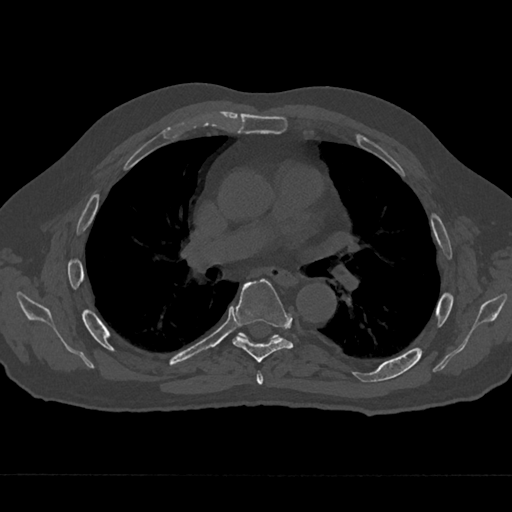
CT including the spine, one axial slice; slice 415 of 797 in the series (ordered by position); reconstruction kernel Br40s/3; bone window (W 1800 / L 400 HU); 512 × 512 image matrix. Patient: male, 75 years. Case-level facts recorded for this patient, not image findings: primary cancer: renal; vertebrae with lytic lesions (as recorded): T4.
Structures marked on this image (semi-automatic segmentation, software-assisted and operator-edited):
- T5 vertebra: bounding box [x1, y1, x2, y2] px = [256, 372, 263, 385]
- T6 vertebra: [232, 279, 294, 362]
- T7 vertebra: [240, 333, 278, 339]